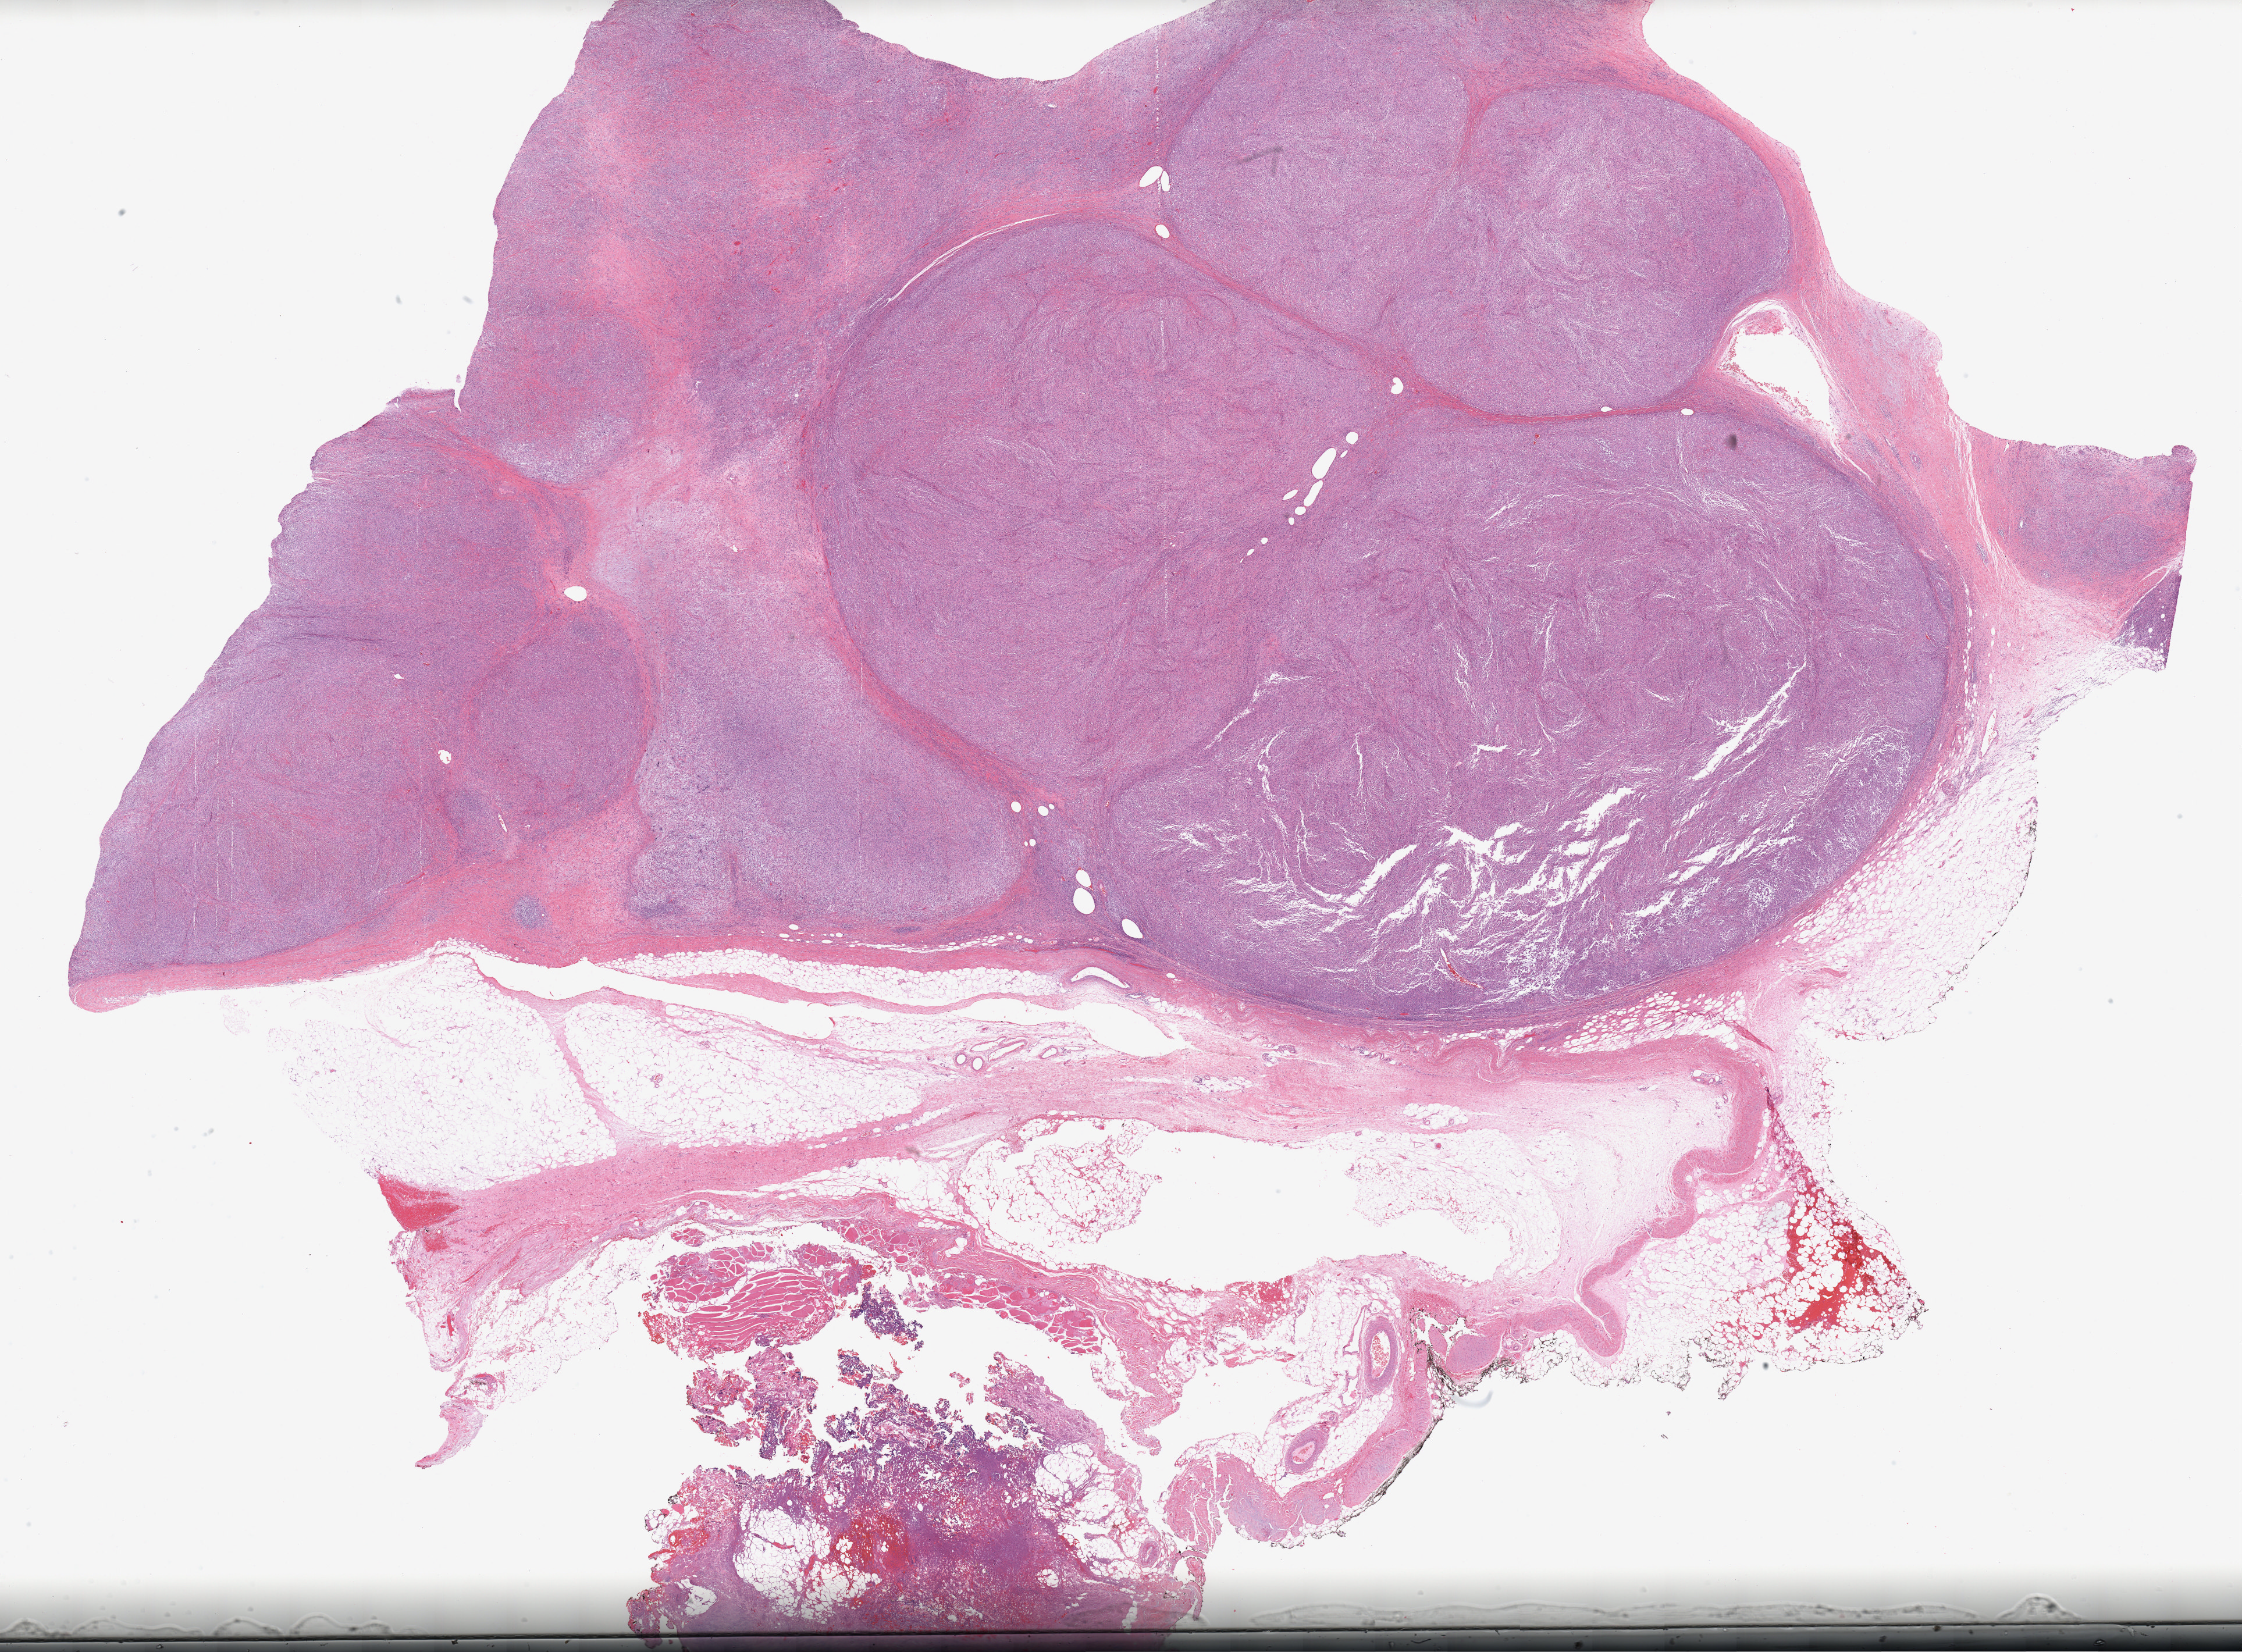
Digitized Hematoxylin and eosin (H&E) stained tissue section (whole slide) — a low-resolution overview of the entire scanned area, about 30.7 x 22.6 mm (slide scanned at 20x), formalin-fixed paraffin-embedded (FFPE) diagnostic section, sample: primary tumour, retroperitoneum and peritoneum. Female patient; age at initial diagnosis 85 years.
• pathologic diagnosis: Dedifferentiated liposarcoma